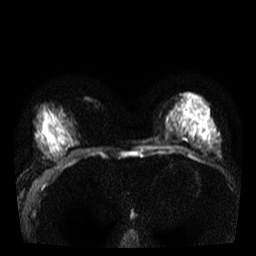
Breast MRI, one axial slice. Position 16 of 40 along the scan axis. Diffusion-weighted series; image 2 of 4 stored at this slice position (different b-values; order by instance number). 3 T. 5 mm slice thickness. 256 × 256 image matrix, field of view 320 × 320 mm. Female patient.
Outlined on this slice (outlined manually by an expert reader):
- tumour on diffusion-weighted imaging: box from (x=189, y=112) to (x=198, y=122) px